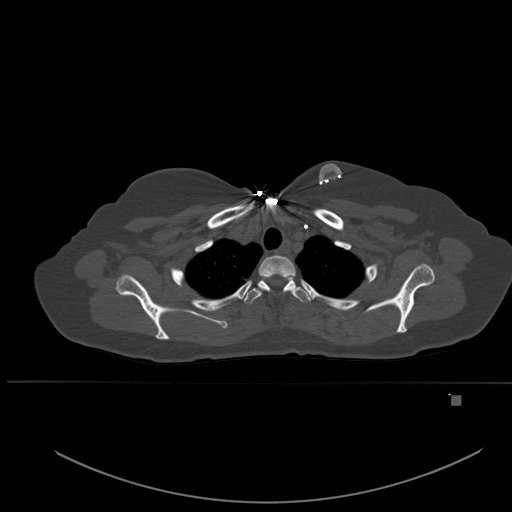
CT including the spine, one axial slice. Position 411 of 651 along the scan axis. Bone window (W 1800 / L 400 HU). 1.5 mm slice thickness. 512 × 512 image matrix. Patient: female, 49 years. From the clinical record (not read from this slice): primary cancer: breast.
Annotated regions visible in this slice (semi-automatic segmentation, software-assisted and operator-edited):
- T1 vertebra: bounding box [x1, y1, x2, y2] px = [258, 255, 296, 278]
- T2 vertebra: [244, 276, 311, 304]